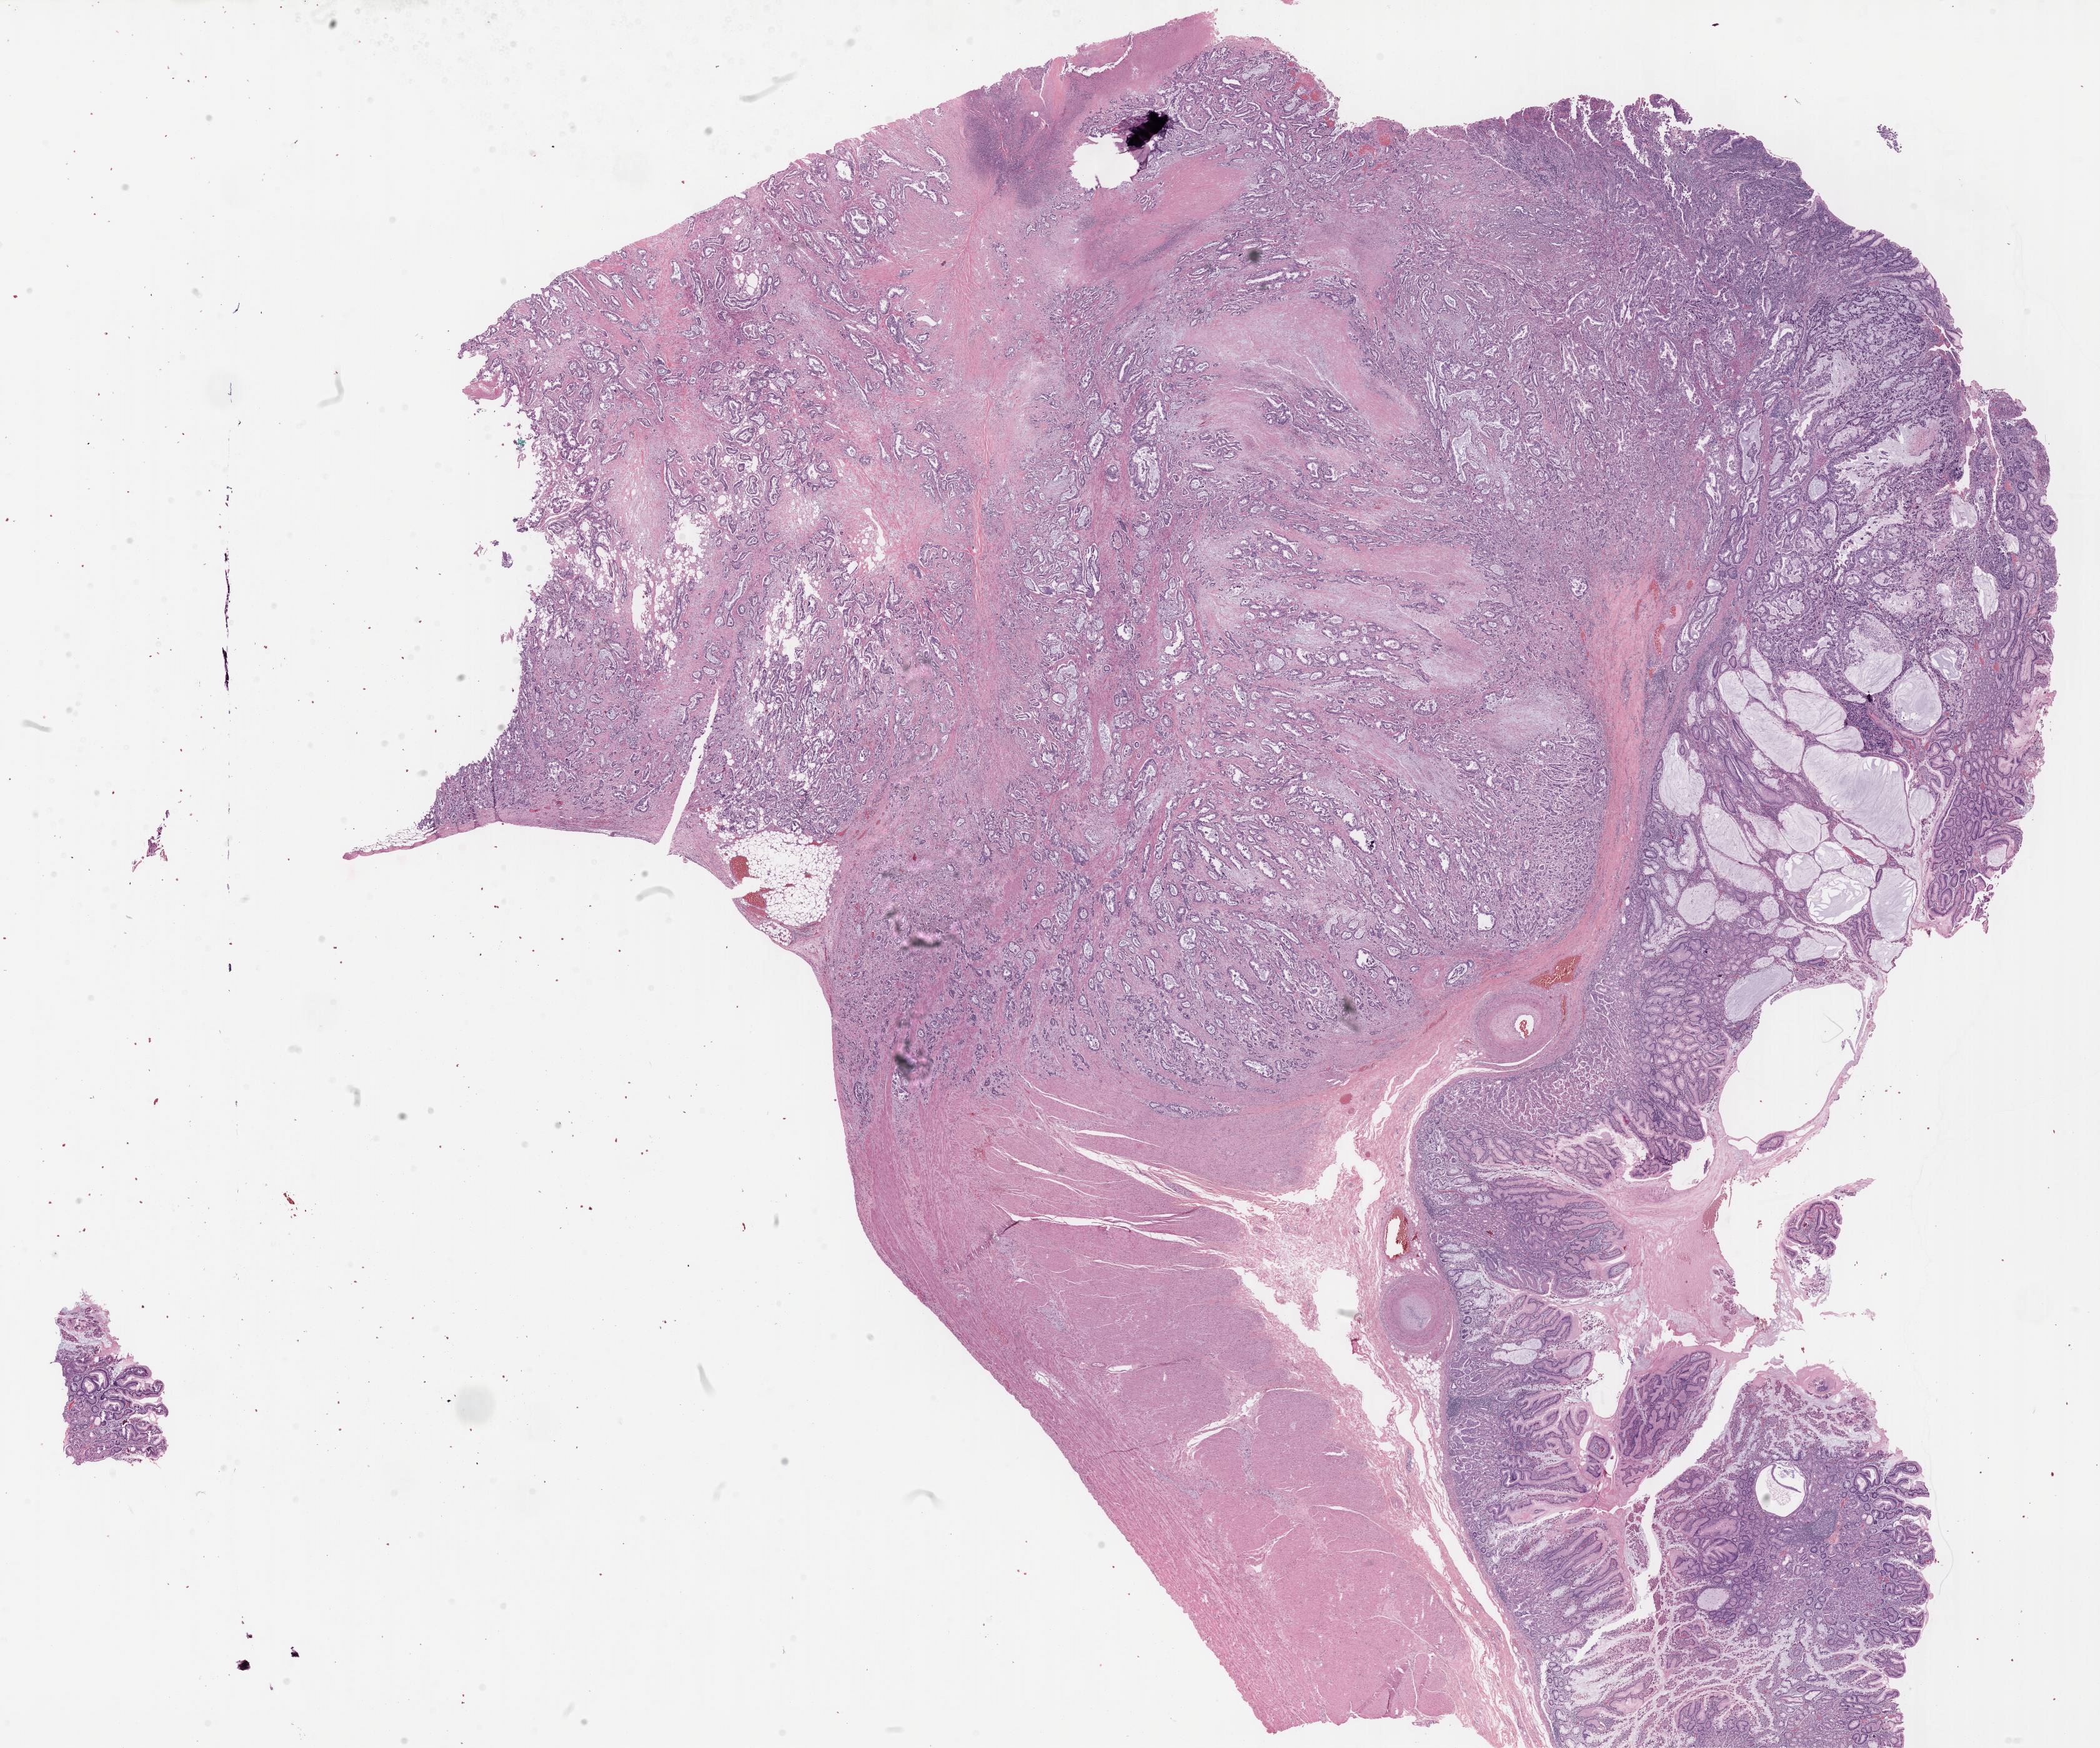
Digitized H&E-stained tissue section (whole slide) — low-resolution overview of the scanned area, about 27.2 x 22.6 mm (acquisition: 40x scan). FFPE section. Sample: primary tumour, stomach. Male patient; age at initial diagnosis 68 years. Histologic grade: G2 (moderately differentiated).
- pathologic diagnosis: Adenocarcinoma, intestinal type
- lymph nodes positive (case pathology): 6 of 34 examined
- AJCC pathologic stage: IIIB (7th edition)